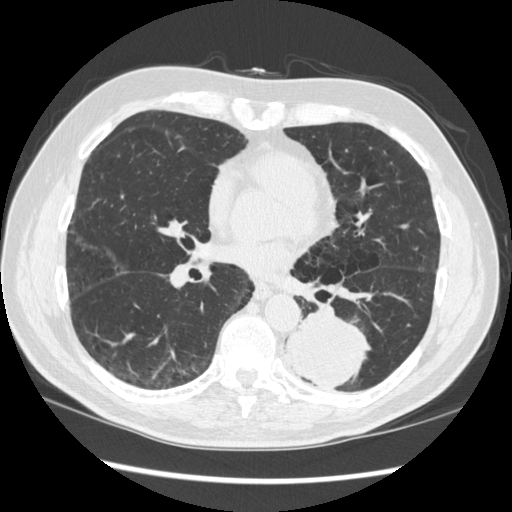
Low-dose screening chest CT, one axial slice; position 151 of 348 along the scan axis; lung window (W 1500 / L -600 HU); 512 × 512 image matrix, field of view 360 × 360 mm.
Structures marked on this image (outlined manually by an expert reader):
- lesion 1 (tumor, lower lobe of left lung): box from (x=285, y=313) to (x=367, y=390) px